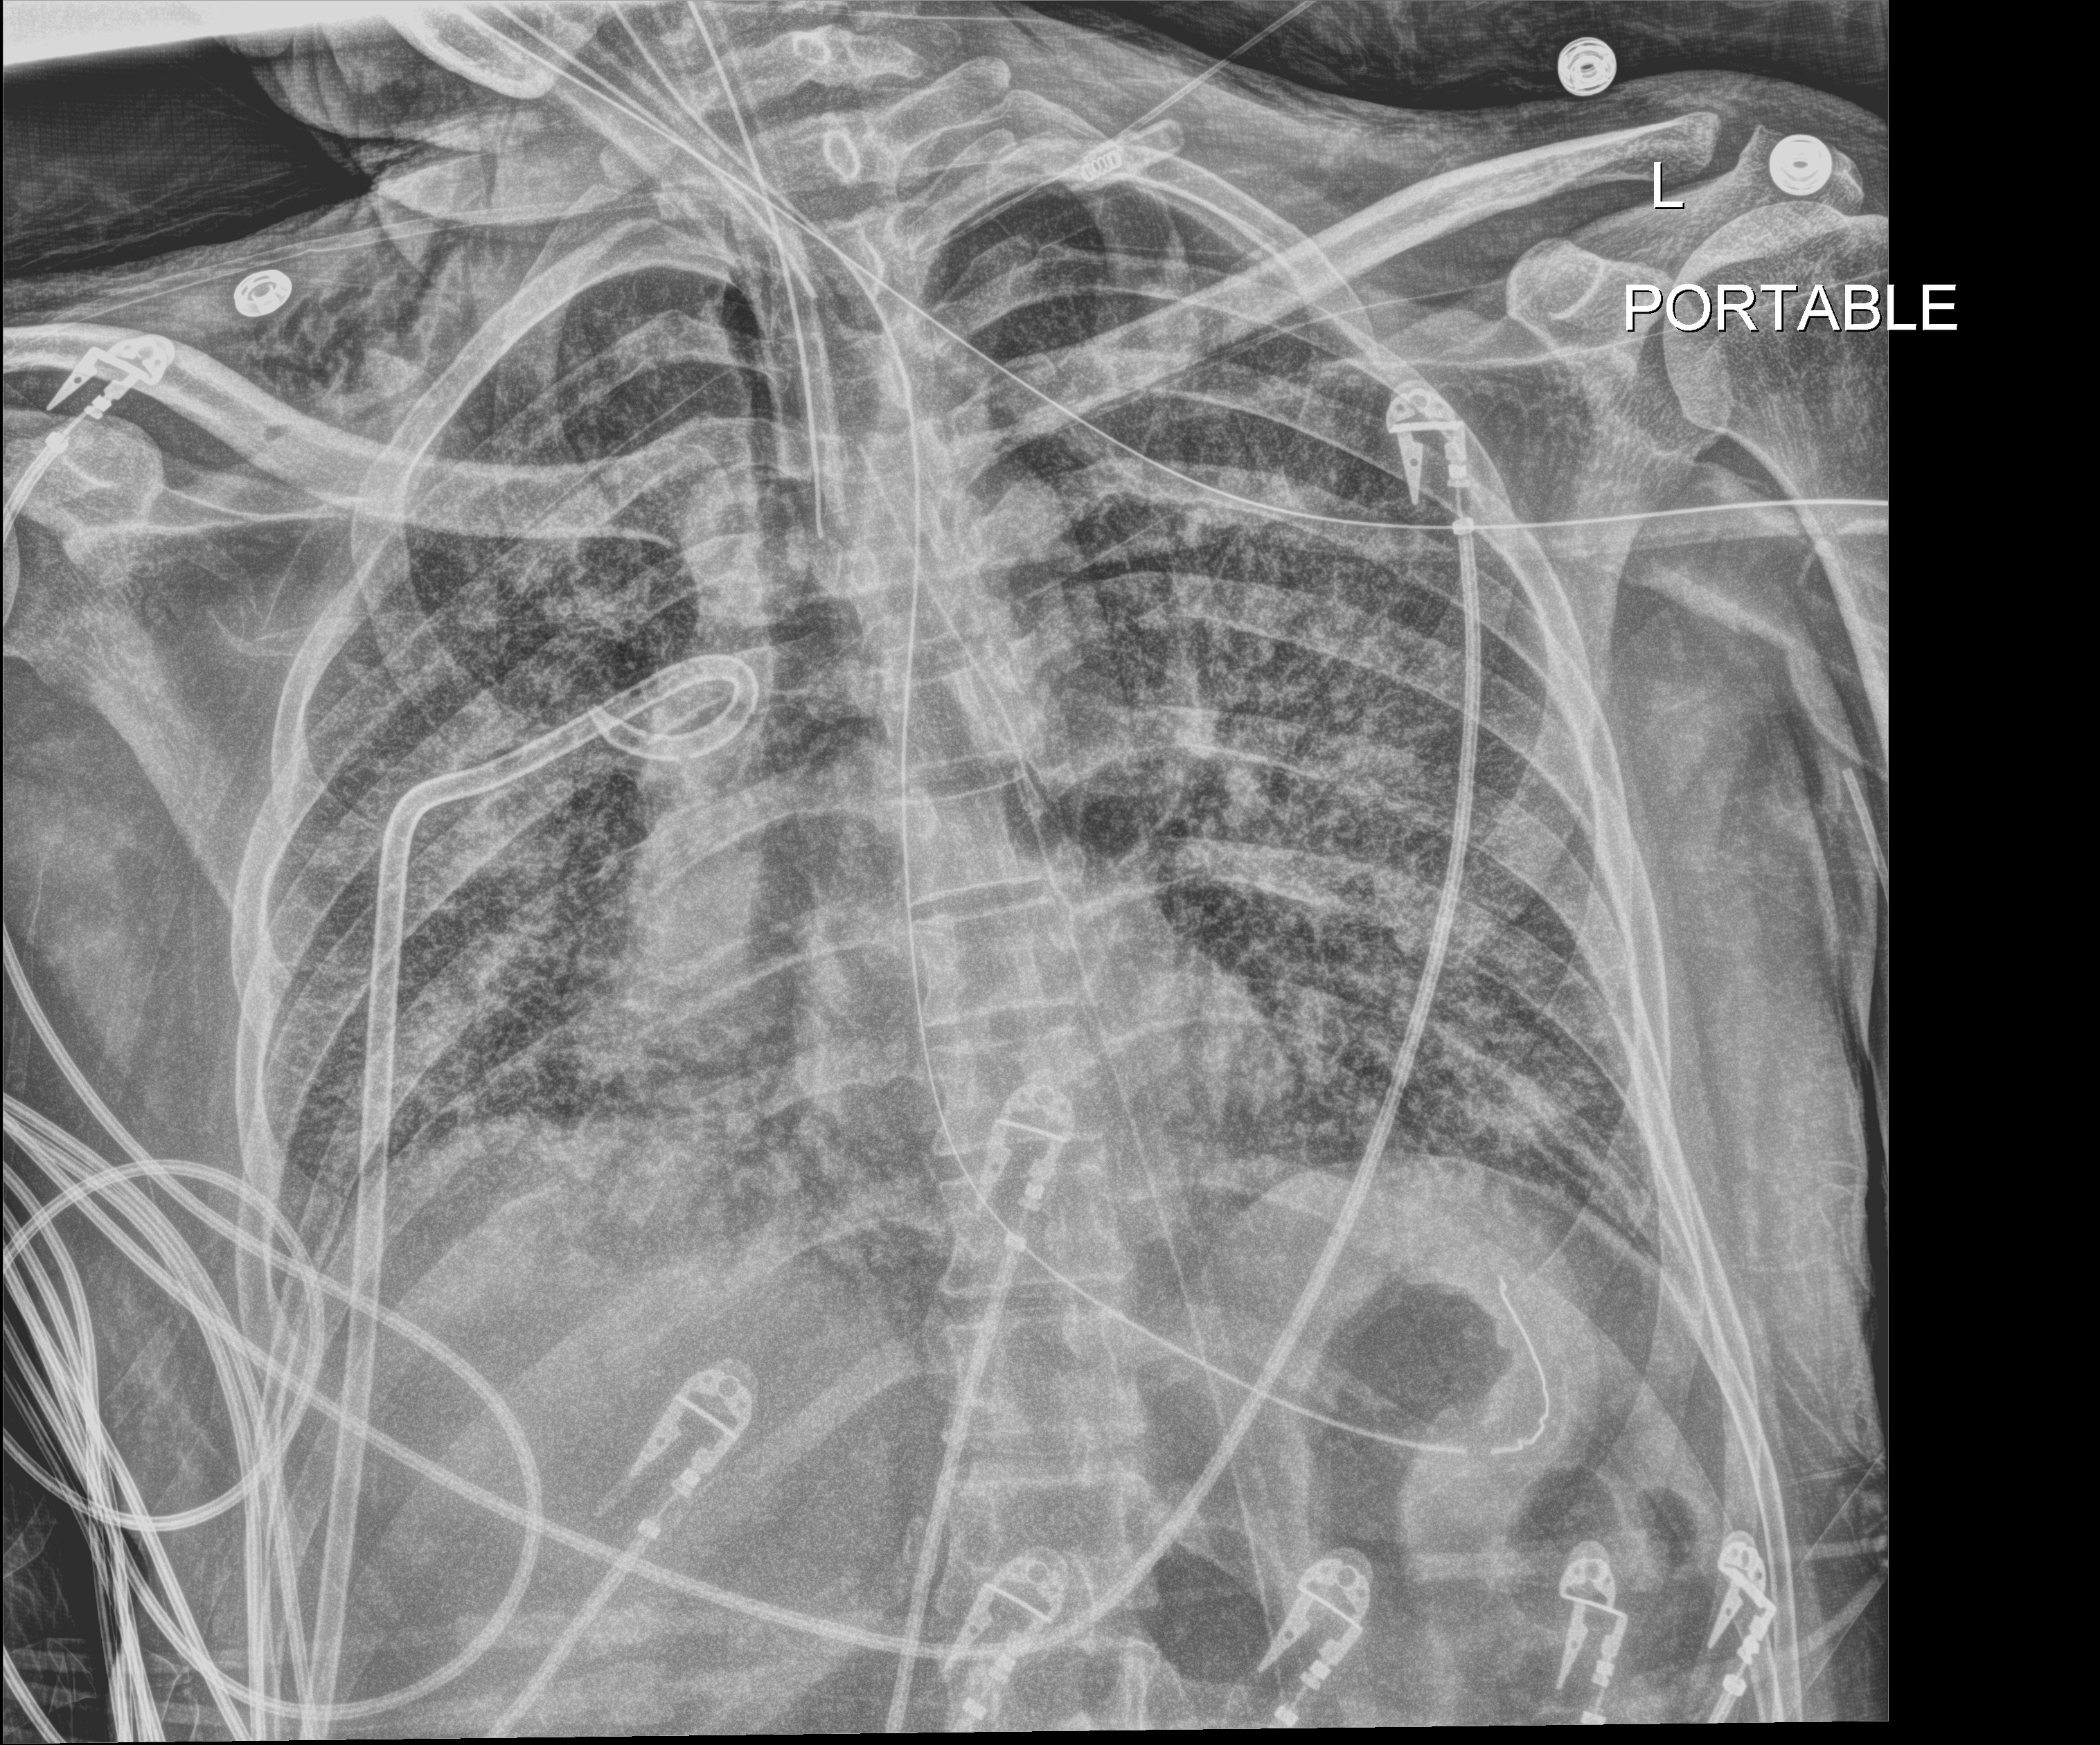
Portable chest radiograph; anteroposterior (AP) projection. Patient hospitalised with COVID-19, aged 18–59 years.
From the hospital-stay record, not from the radiograph (when in the stay this image was taken is not recorded): admitted to intensive care during this hospital stay: yes.